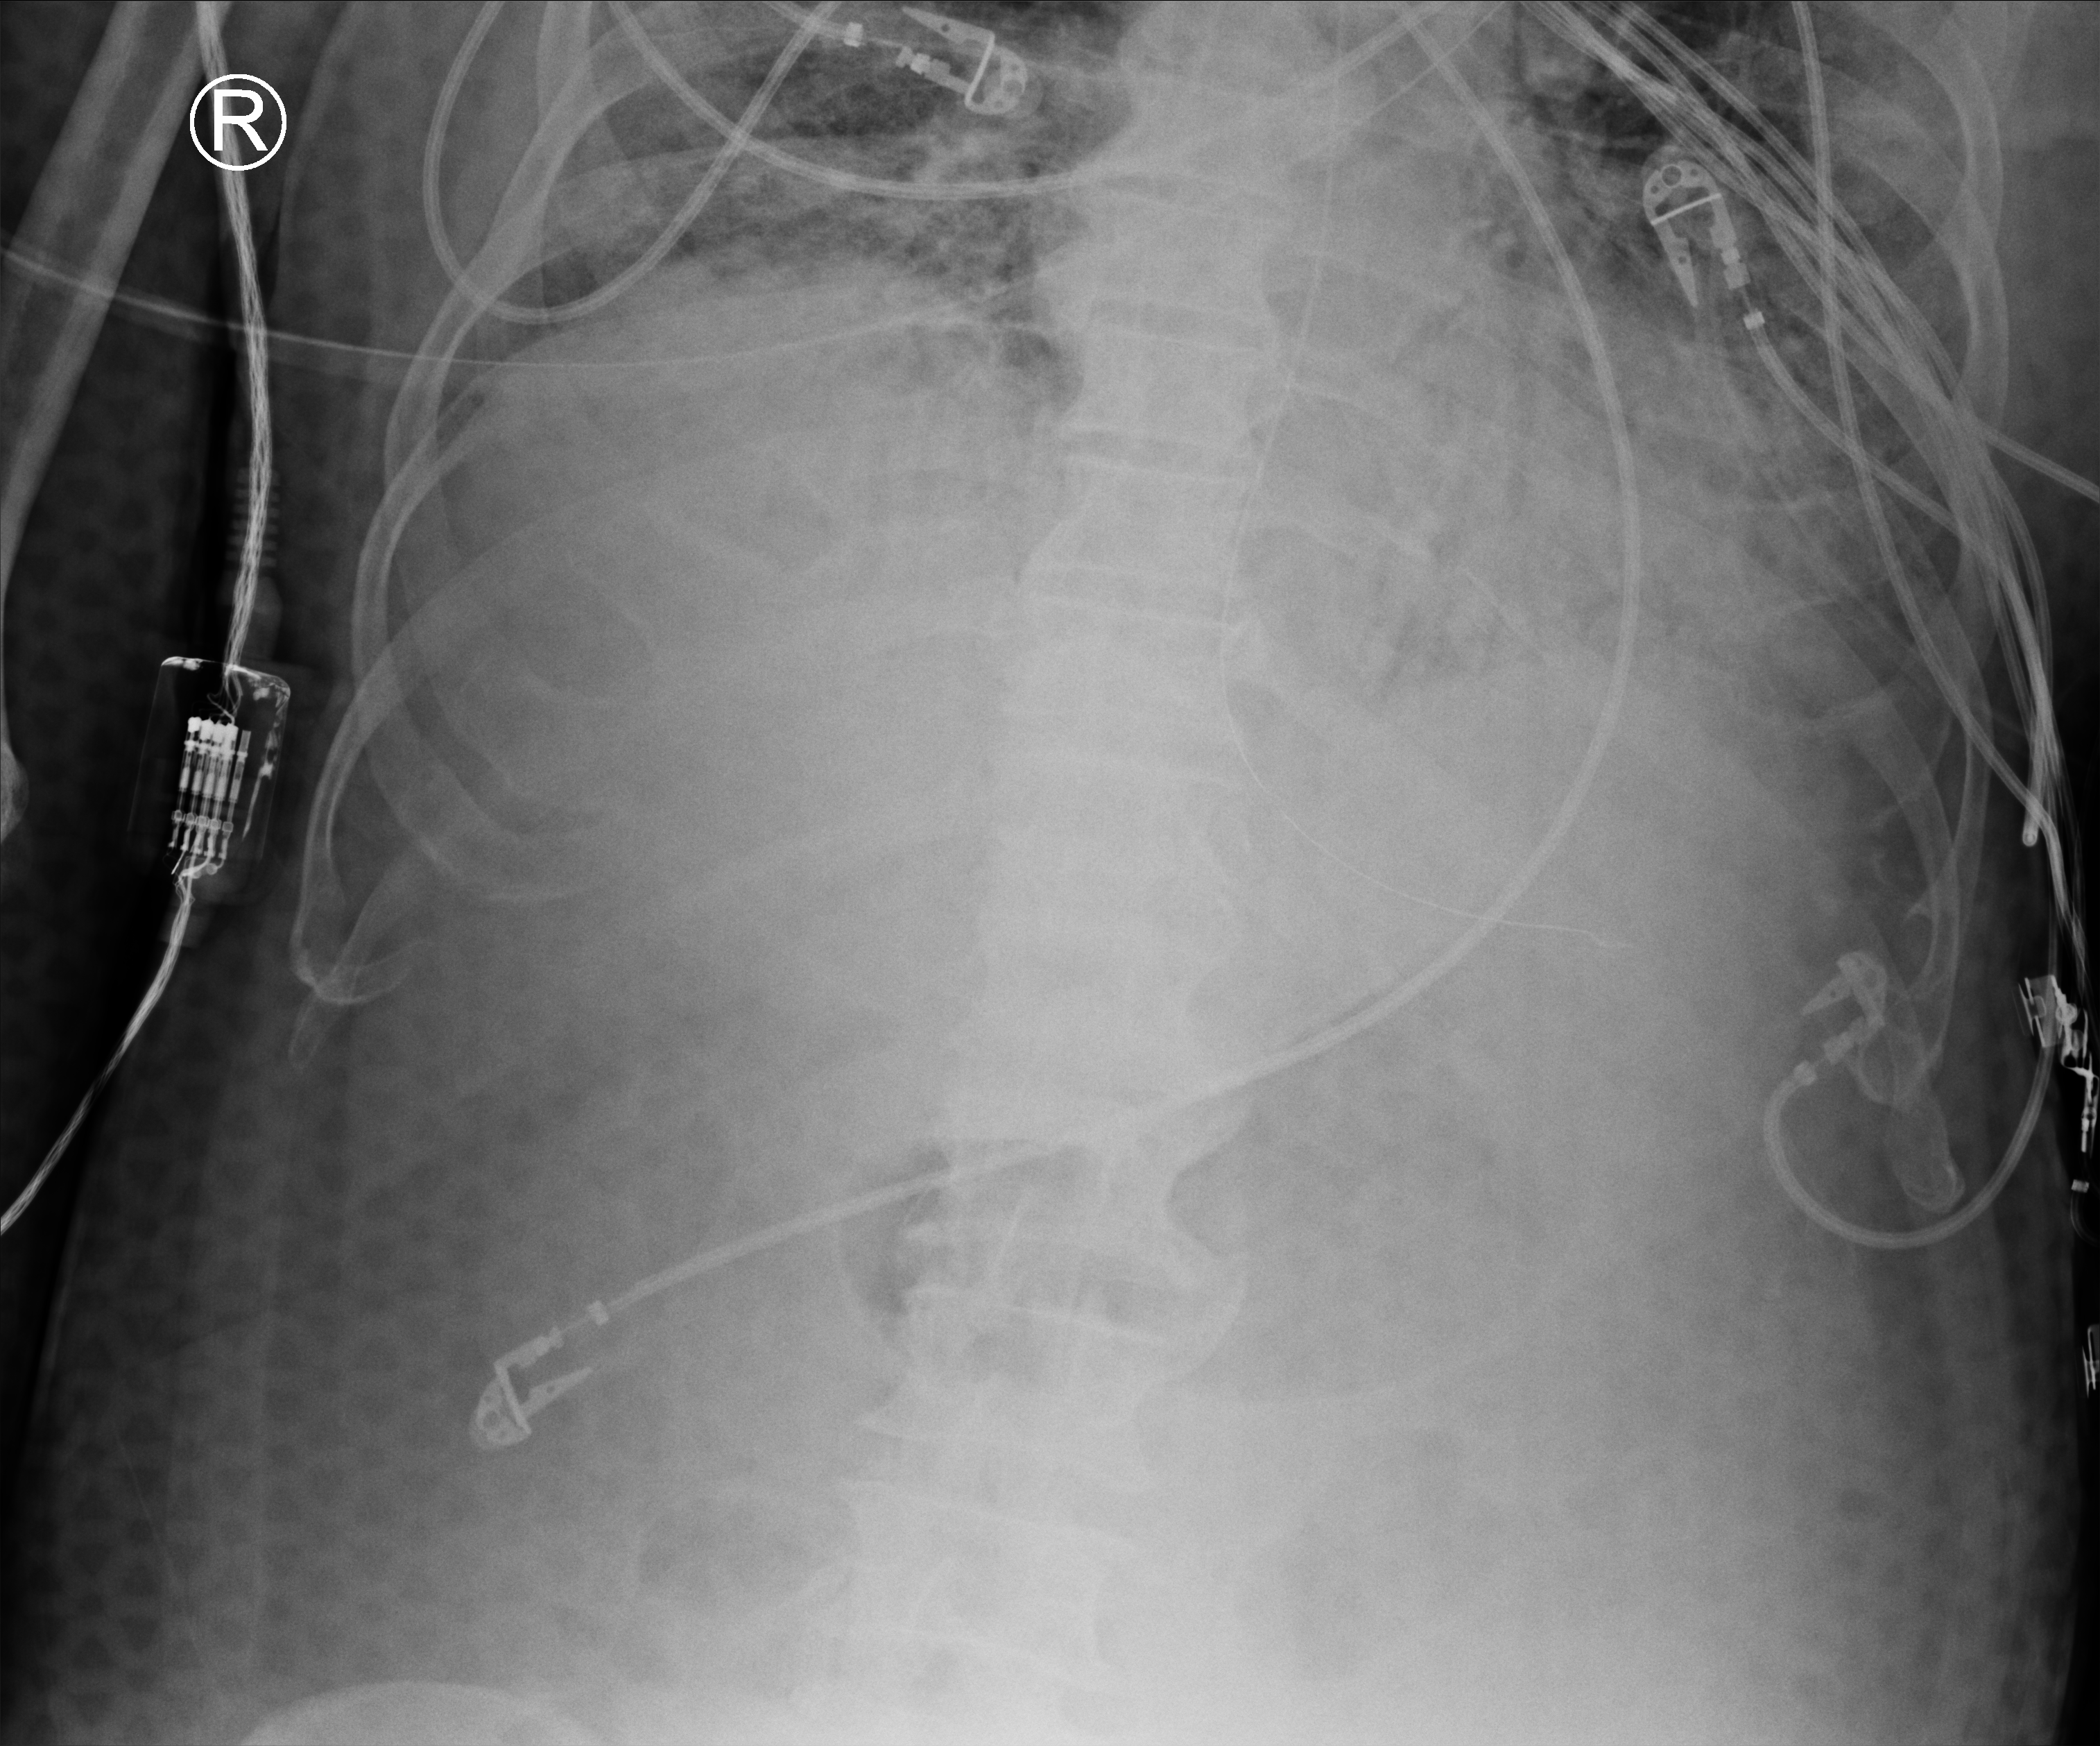
Portable chest radiograph; anteroposterior (AP) projection. Patient hospitalised with COVID-19; male, aged 75–90 years.
From the hospital-stay record, not from the radiograph (when in the stay this image was taken is not recorded): mechanically ventilated during this hospital stay: yes; admitted to intensive care during this hospital stay: yes; length of hospital stay: 33 days.